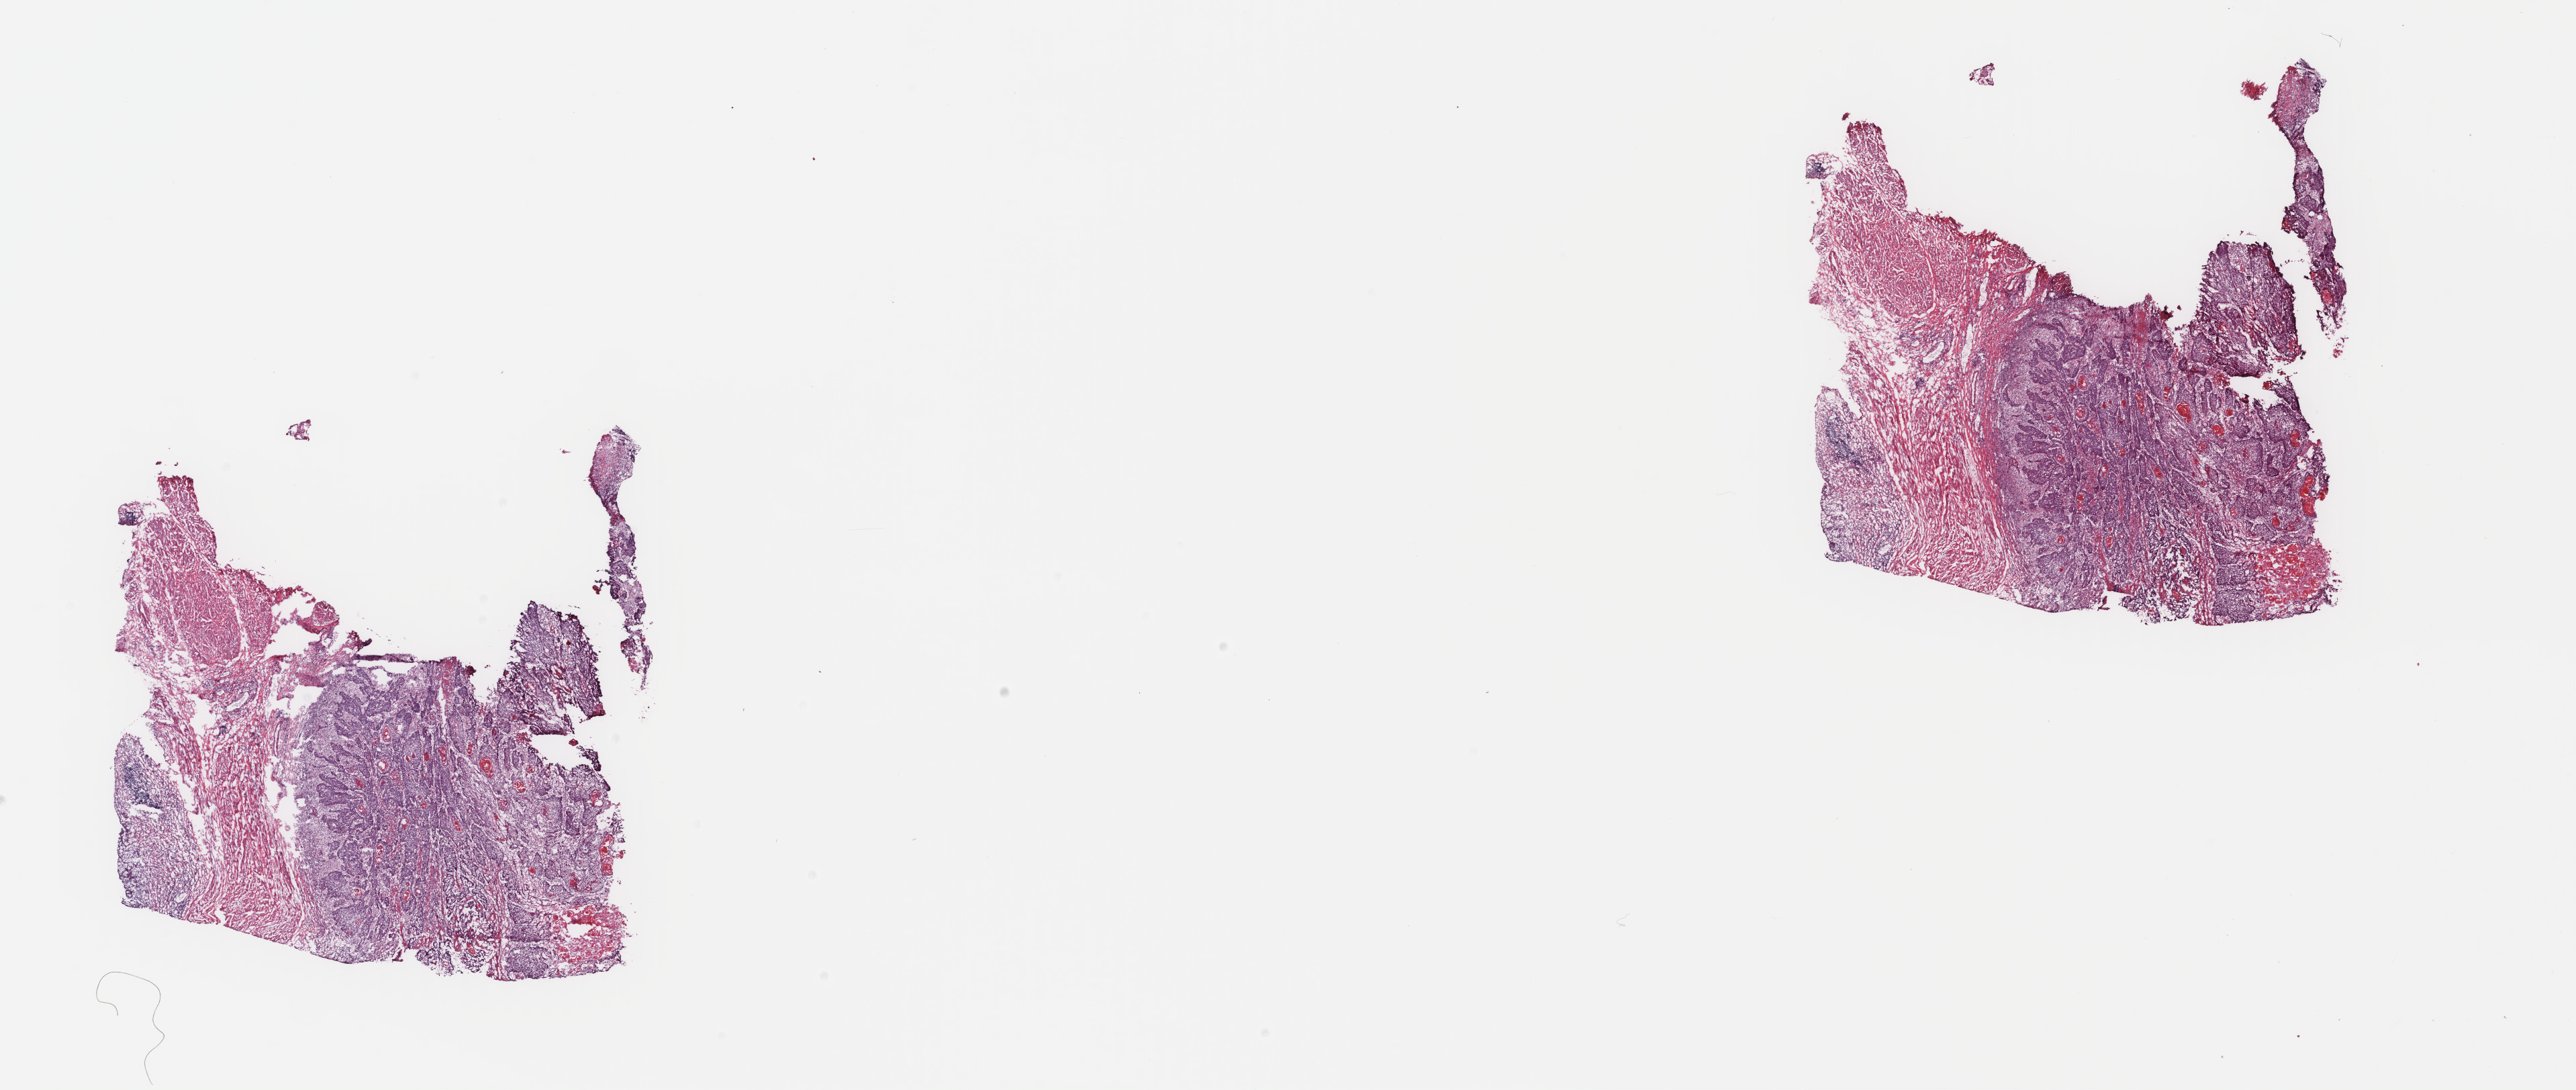
Hematoxylin and eosin (H&E) stained whole-slide image — a low-resolution overview of the entire scanned area, about 30.5 x 12.9 mm (from a 40x scan), frozen section from the top of the tissue portion, sample: primary tumour, bladder. Female, age 55 years at initial diagnosis. Histologic grade: high grade. Composition of this section per pathologist review: tumour cells 55%, tumour nuclei 80%, normal cells 0%, stromal cells 35%, necrosis 10%. Infiltration values recorded for this section: lymphocyte infiltration 2%, monocyte infiltration 0%, neutrophil infiltration 0%.
* AJCC pathologic stage: III (7th edition)
* lymph nodes positive (case pathology): 0 of 27 examined
* diagnosis: Transitional cell carcinoma (lateral wall of bladder)